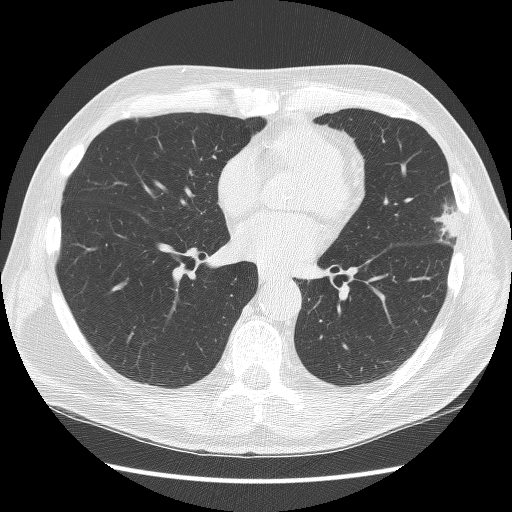
Low-dose screening chest CT, axial slice, third screening round (two years after baseline), lung window (W 1500 / L -600 HU), 2.5 mm slice thickness, lung (sharp) reconstruction kernel (BONE), 512 × 512 image matrix, field of view 350 × 350 mm. Male participant, aged 67 years at enrolment. Former smoker at enrolment.
- Expert reader's lesion annotation, box from (x=409, y=190) to (x=472, y=262) px.
- Screening reader's record for this exam (one nodule recorded; not confirmed to be the boxed lesion): non-calcified nodule or mass ≥4 mm, left upper lobe, 22 × 17 mm, poorly defined margins, soft tissue attenuation, pre-existing on the prior screen: yes; interval growth: yes.
- Participant outcome: lung cancer diagnosed 72 days after this screen — squamous cell carcinoma, NOS, left upper lobe, moderately differentiated (G2), stage IB (AJCC 6th edition), 25 mm at pathology.